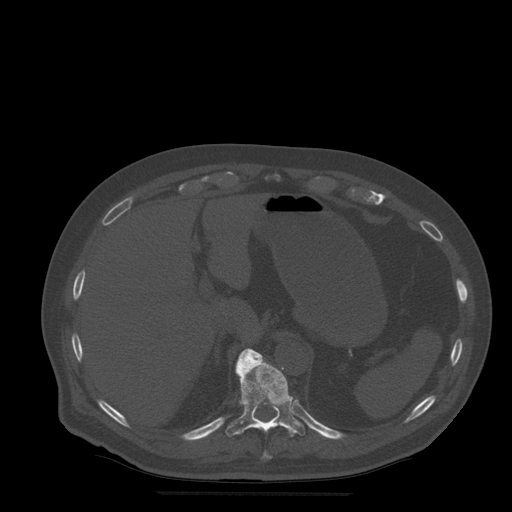
CT including the spine, one axial slice; position 248 of 522 along the scan axis; bone window (W 1800 / L 400 HU); 1.25 mm slice thickness; 512 × 512 image matrix, field of view 420 × 420 mm. Patient age 72 years. From the clinical record (not read from this slice): primary cancer: prostate.
Annotated regions visible in this slice (semi-automatic segmentation, software-assisted and operator-edited):
- T10 vertebra: bounding box (x1, y1, x2, y2) in pixels: (264, 452, 272, 459)
- T11 vertebra: (226, 348, 305, 437)